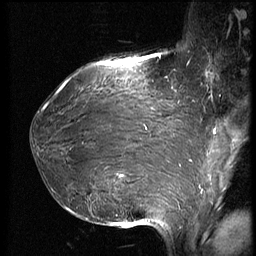
Breast MRI (dynamic contrast-enhanced), one sagittal slice; dynamic contrast-enhanced series, image 2 of 3 at this slice position (ordered by acquisition); 1.5 T; TE 4.2 ms, TR 8.9 ms; 256 × 256 image matrix, field of view 200 × 200 mm. Patient: female, 39 years. Case-level facts recorded for this patient, not image findings: setting: breast cancer imaged before/during neoadjuvant chemotherapy; receptor status: HER2-positive.
Structures marked on this image (semi-automatically segmented with operator editing):
- analysis volume of interest (the breast-tissue region the enhancement analysis was run in; not a lesion): bounding box [x1, y1, x2, y2] px = [32, 75, 188, 218]
- tumour enhancement mask (voxels above the 140 % enhancement threshold inside the analysis volume of interest): [57, 80, 147, 211]